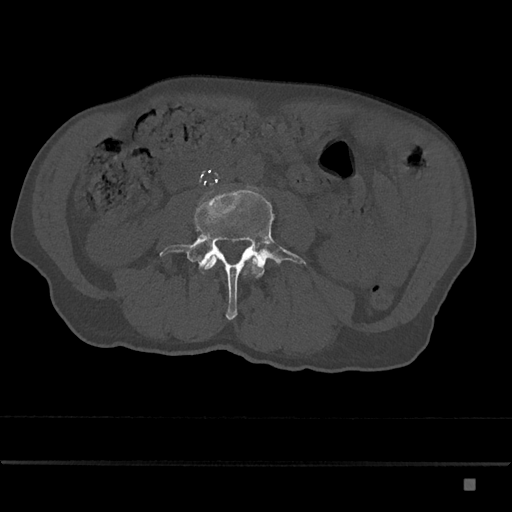
CT including the spine, one axial slice; slice 352 of 797 in the series (ordered by position); 120 kVp; bone window (W 1800 / L 400 HU); 0.5 mm slice thickness; 512 × 512 image matrix. Patient: male, 72 years. From the clinical record (not read from this slice): primary cancer: prostate.
Structures marked on this image (semi-automatic segmentation, software-assisted and operator-edited):
- L3 vertebra: bounding box [x1, y1, x2, y2] px = [204, 256, 258, 270]
- L4 vertebra: [160, 189, 306, 320]